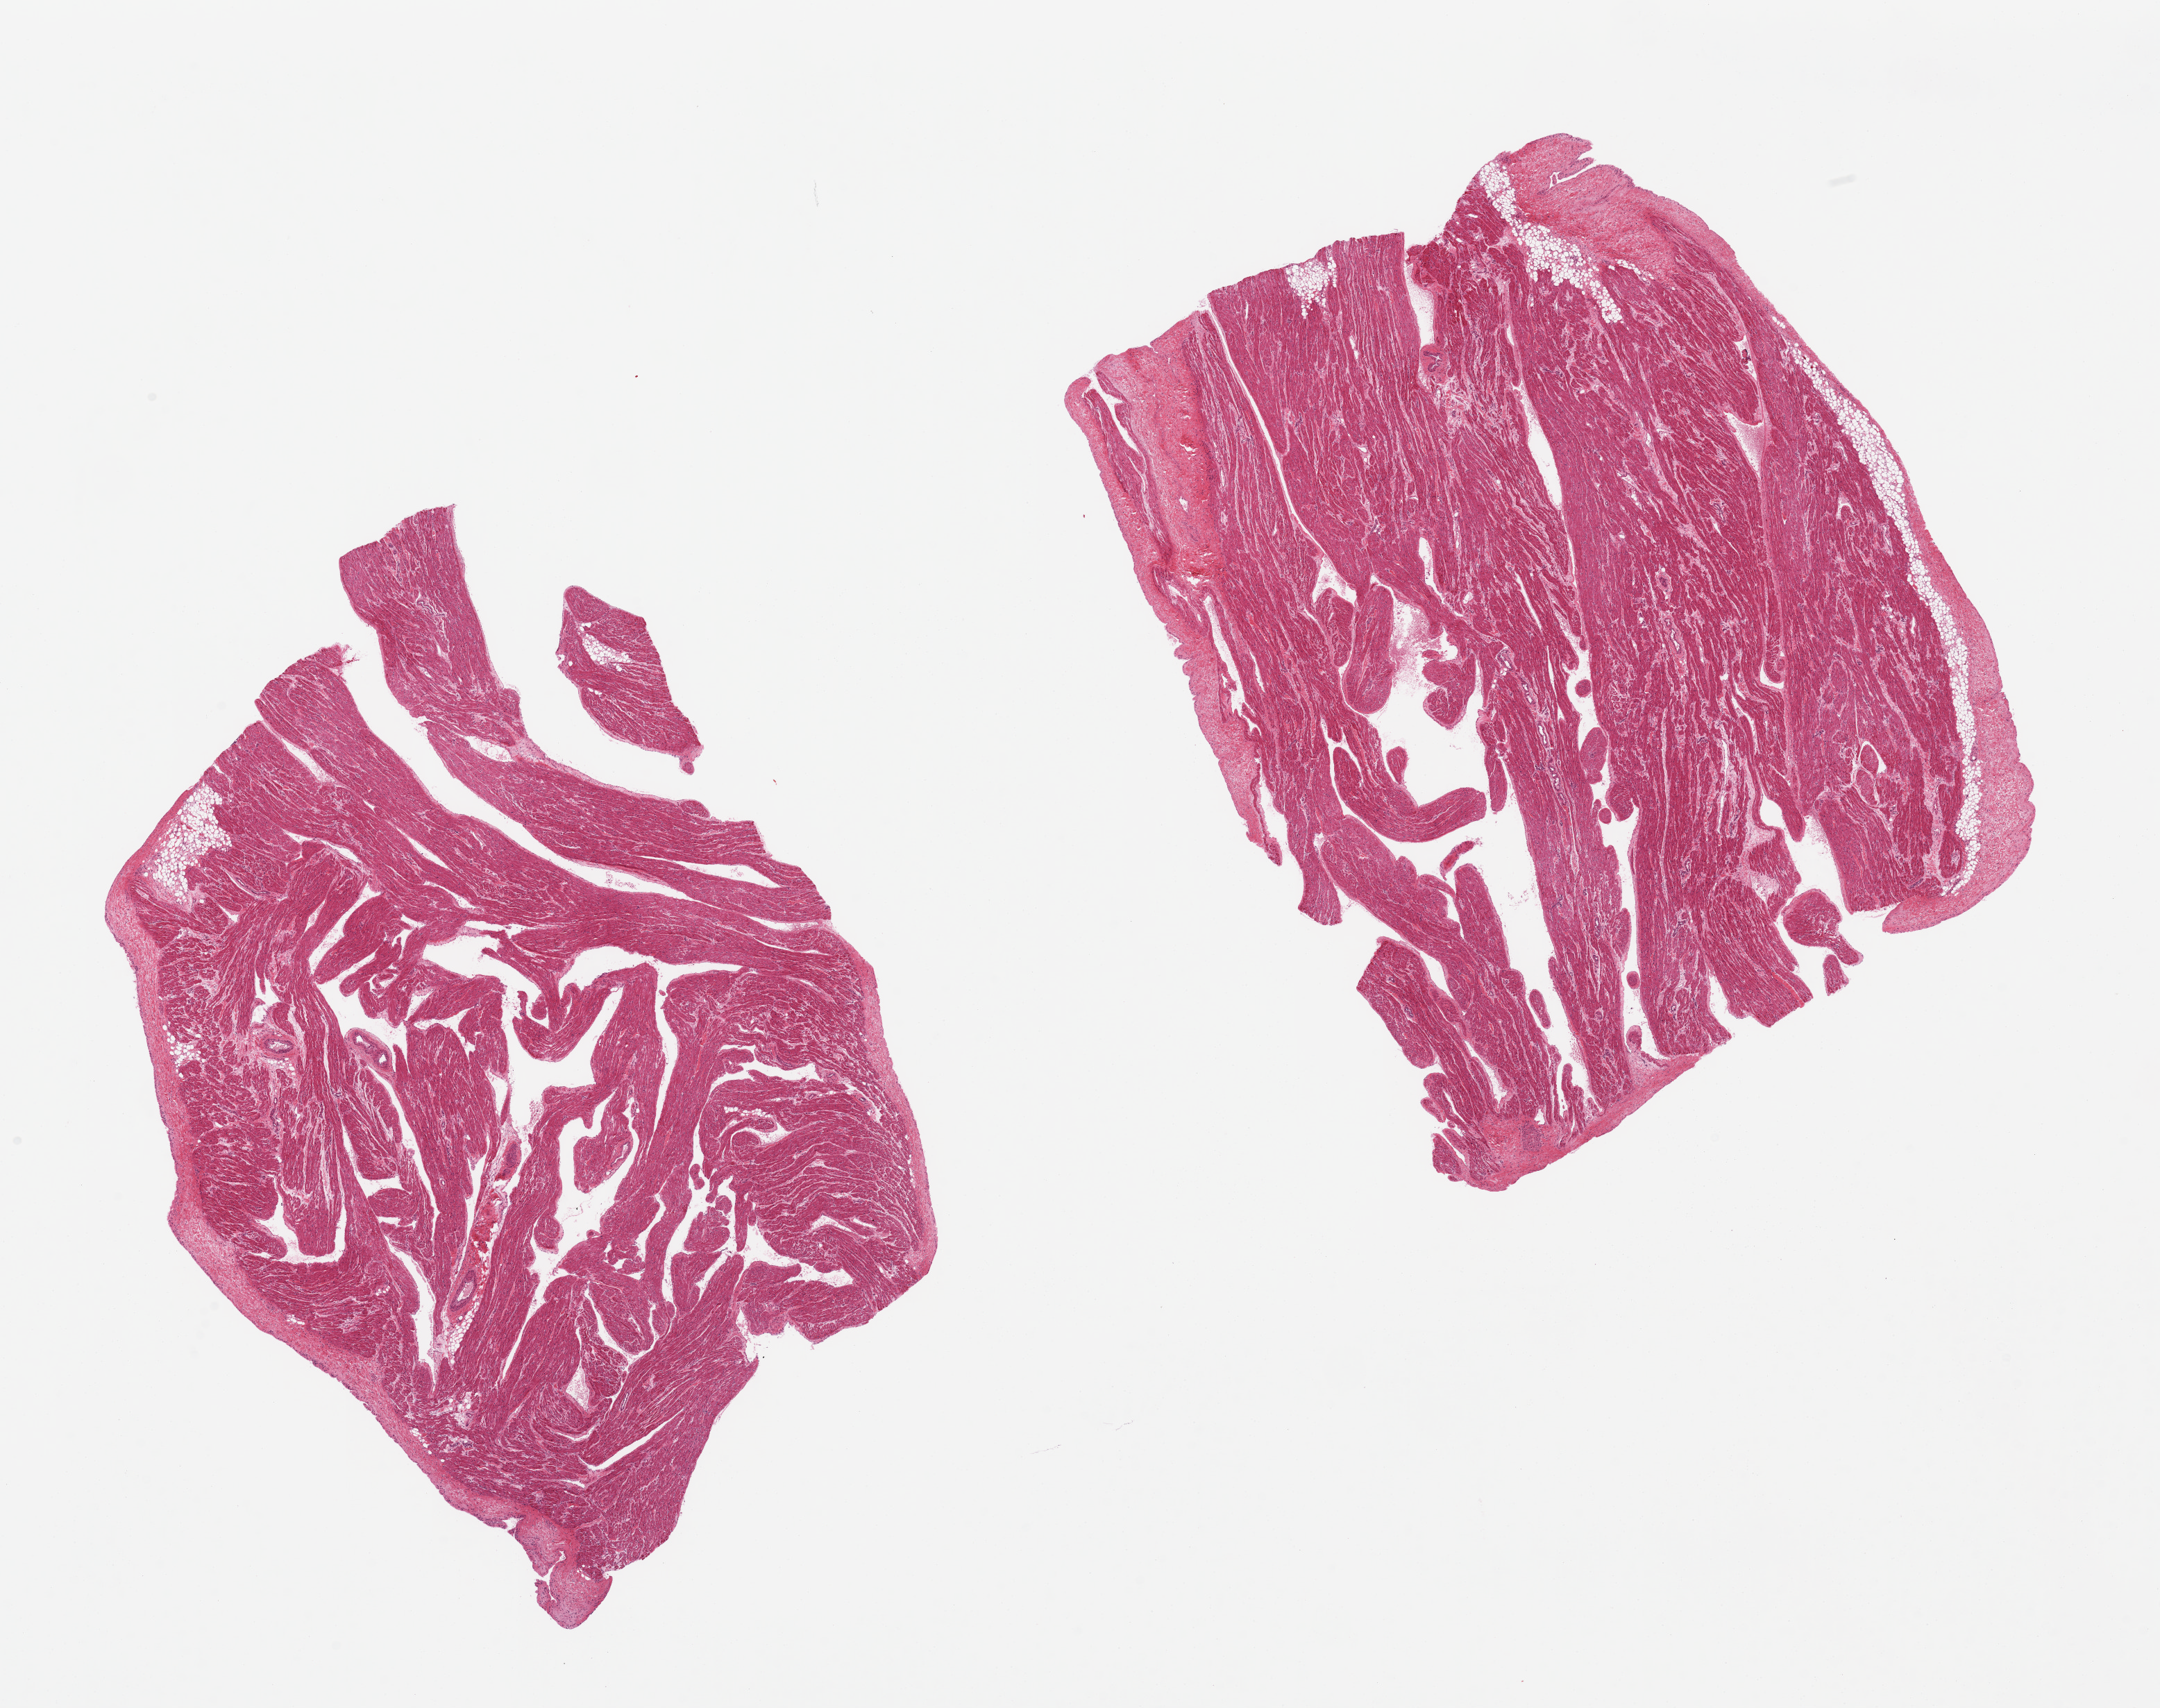
Digitized H&E-stained section — low-resolution overview of the scanned area, about 24.6 x 19.5 mm, PAXgene-fixed, paraffin-embedded tissue, sampled site (target tissue): auricular appendage, donor tissue sample. Donor sex: female.
Pathologist's review note for this sample: 2 pieces, no abnormalities.